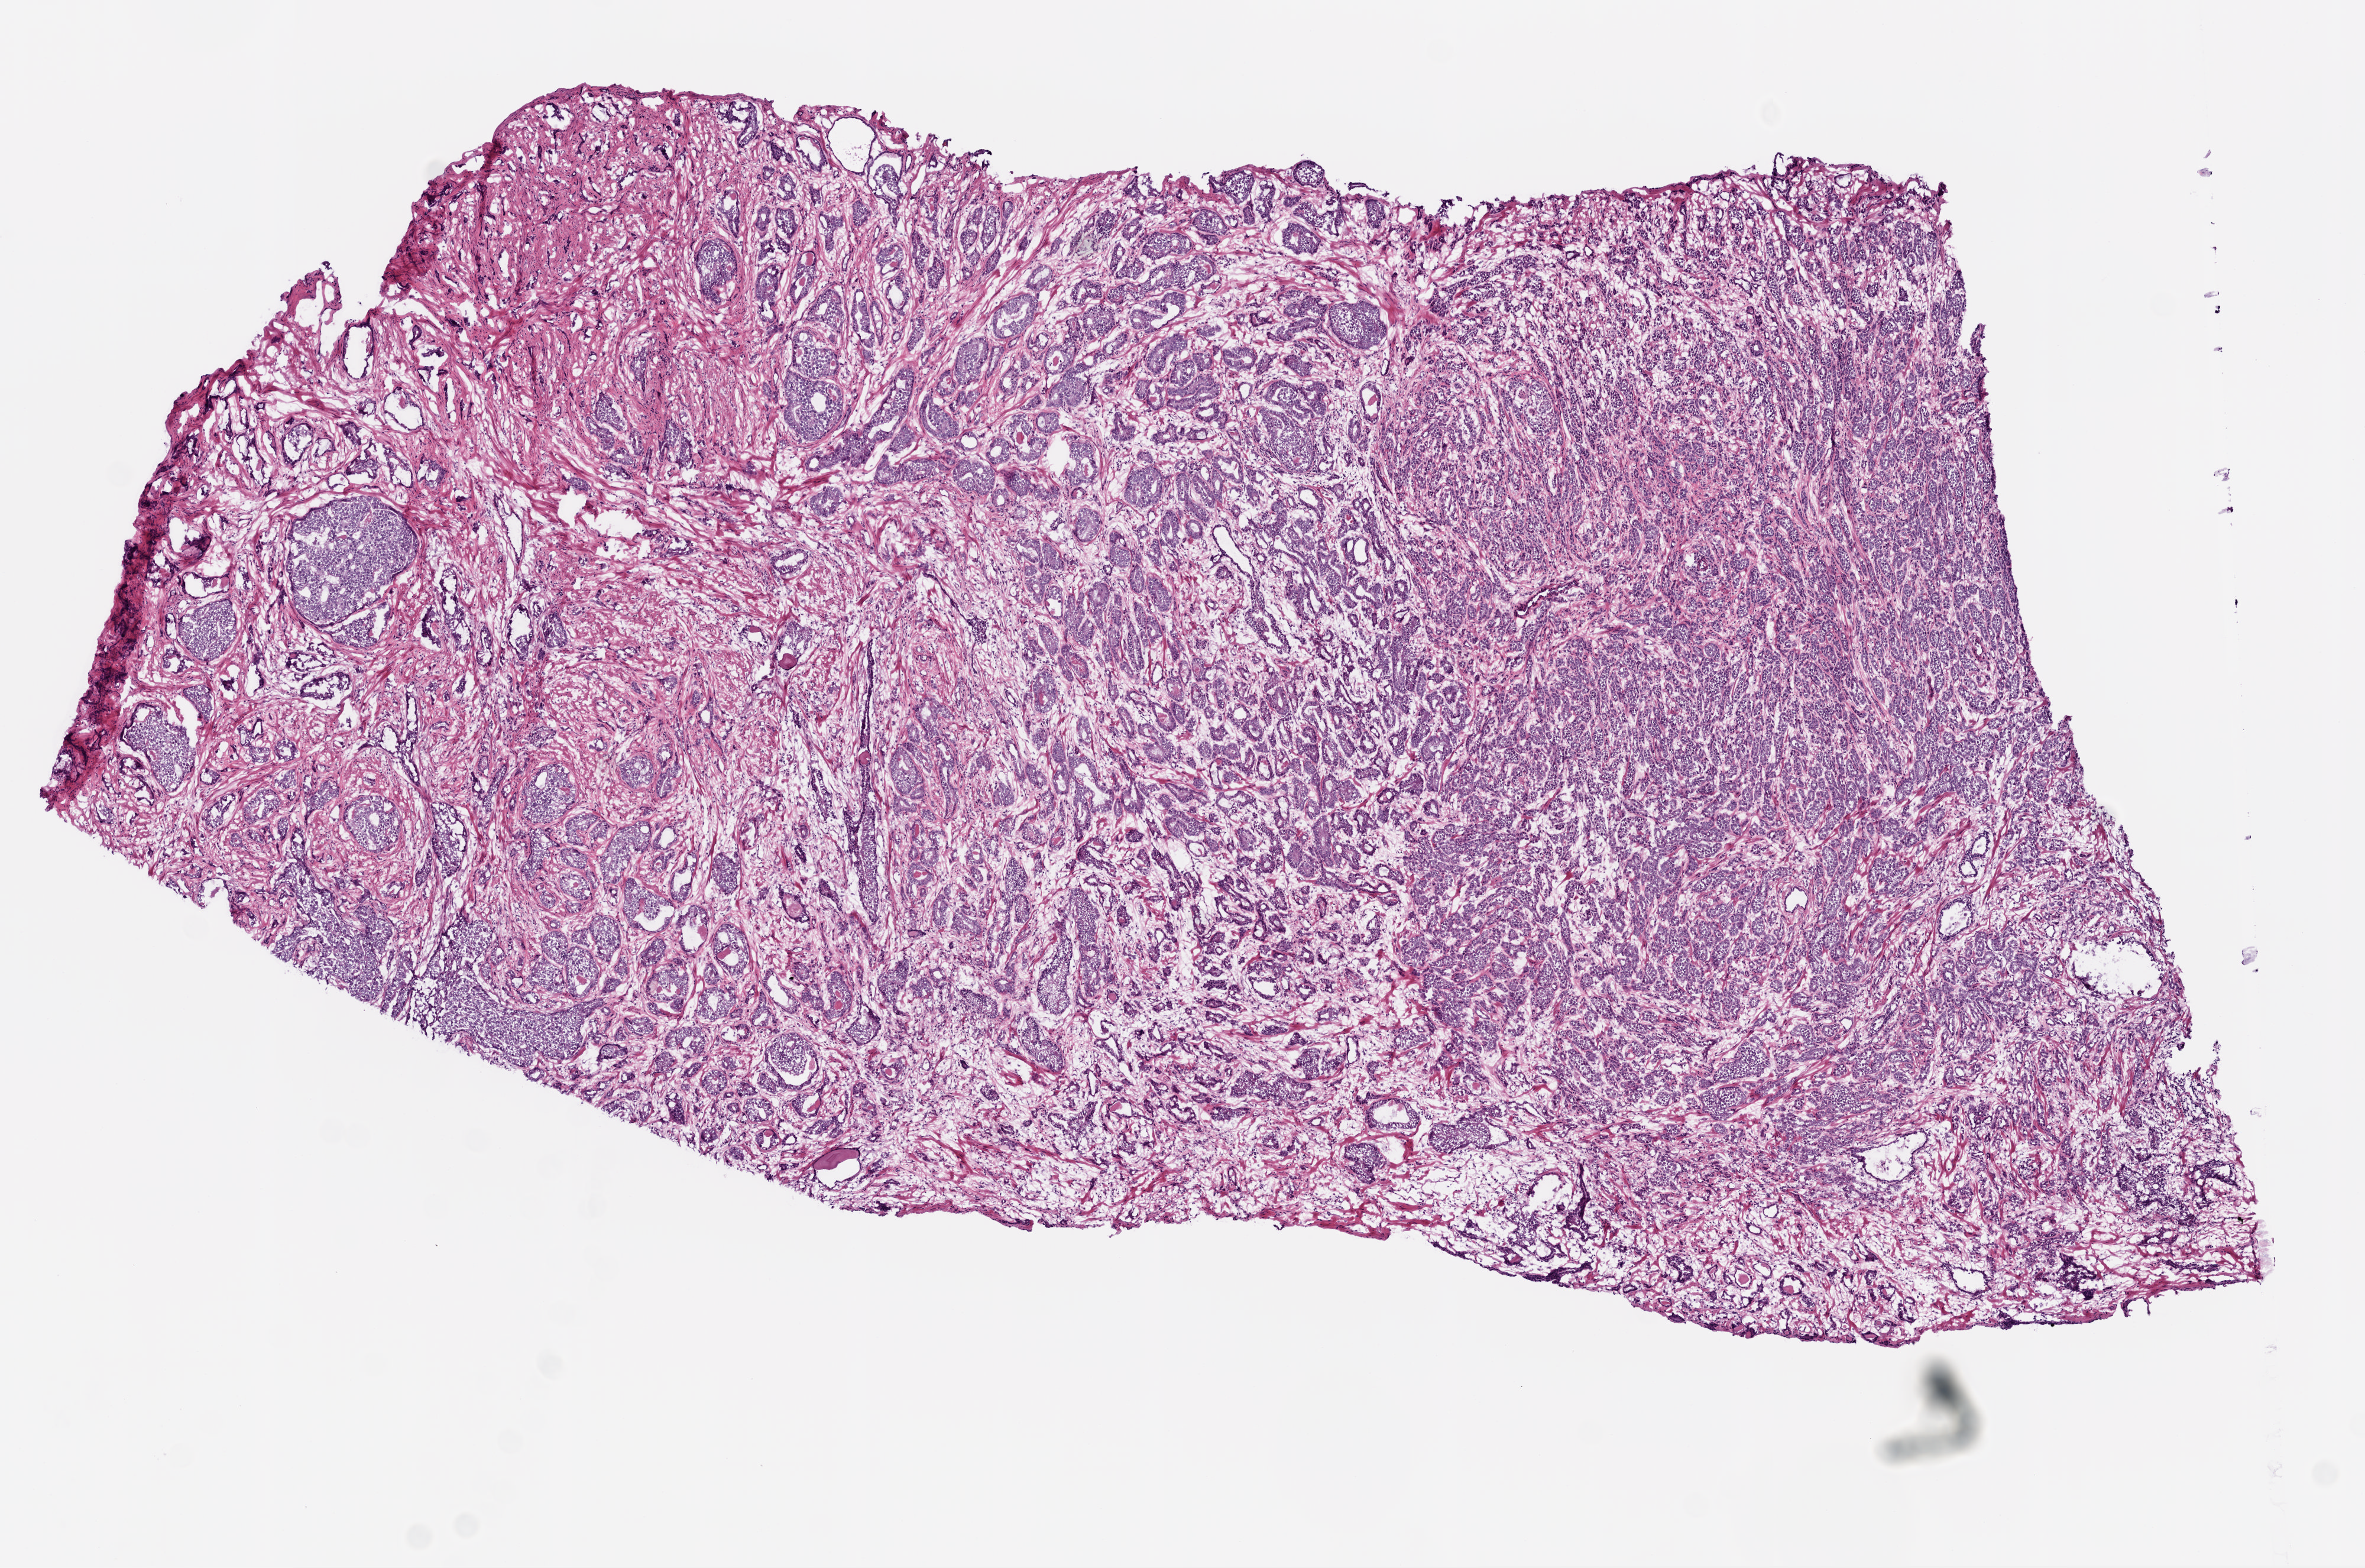
Hematoxylin and eosin (H&E) stained whole-slide image — whole scanned area (about 8.0 x 5.3 mm, acquisition: 20x scan) shown as a low-resolution overview, frozen section, primary tumour sample from the prostate. Male, age 66 years at initial diagnosis. Gleason score: 7 (4+3). Composition of this section per pathologist review: tumour cells 75%, tumour nuclei 75%, normal cells 10%, stromal cells 15%, necrosis 0%. Infiltration values recorded for this section: lymphocyte infiltration 0%, monocyte infiltration 0%, neutrophil infiltration 0%.
Diagnosis: Acinar cell carcinoma (prostate gland).